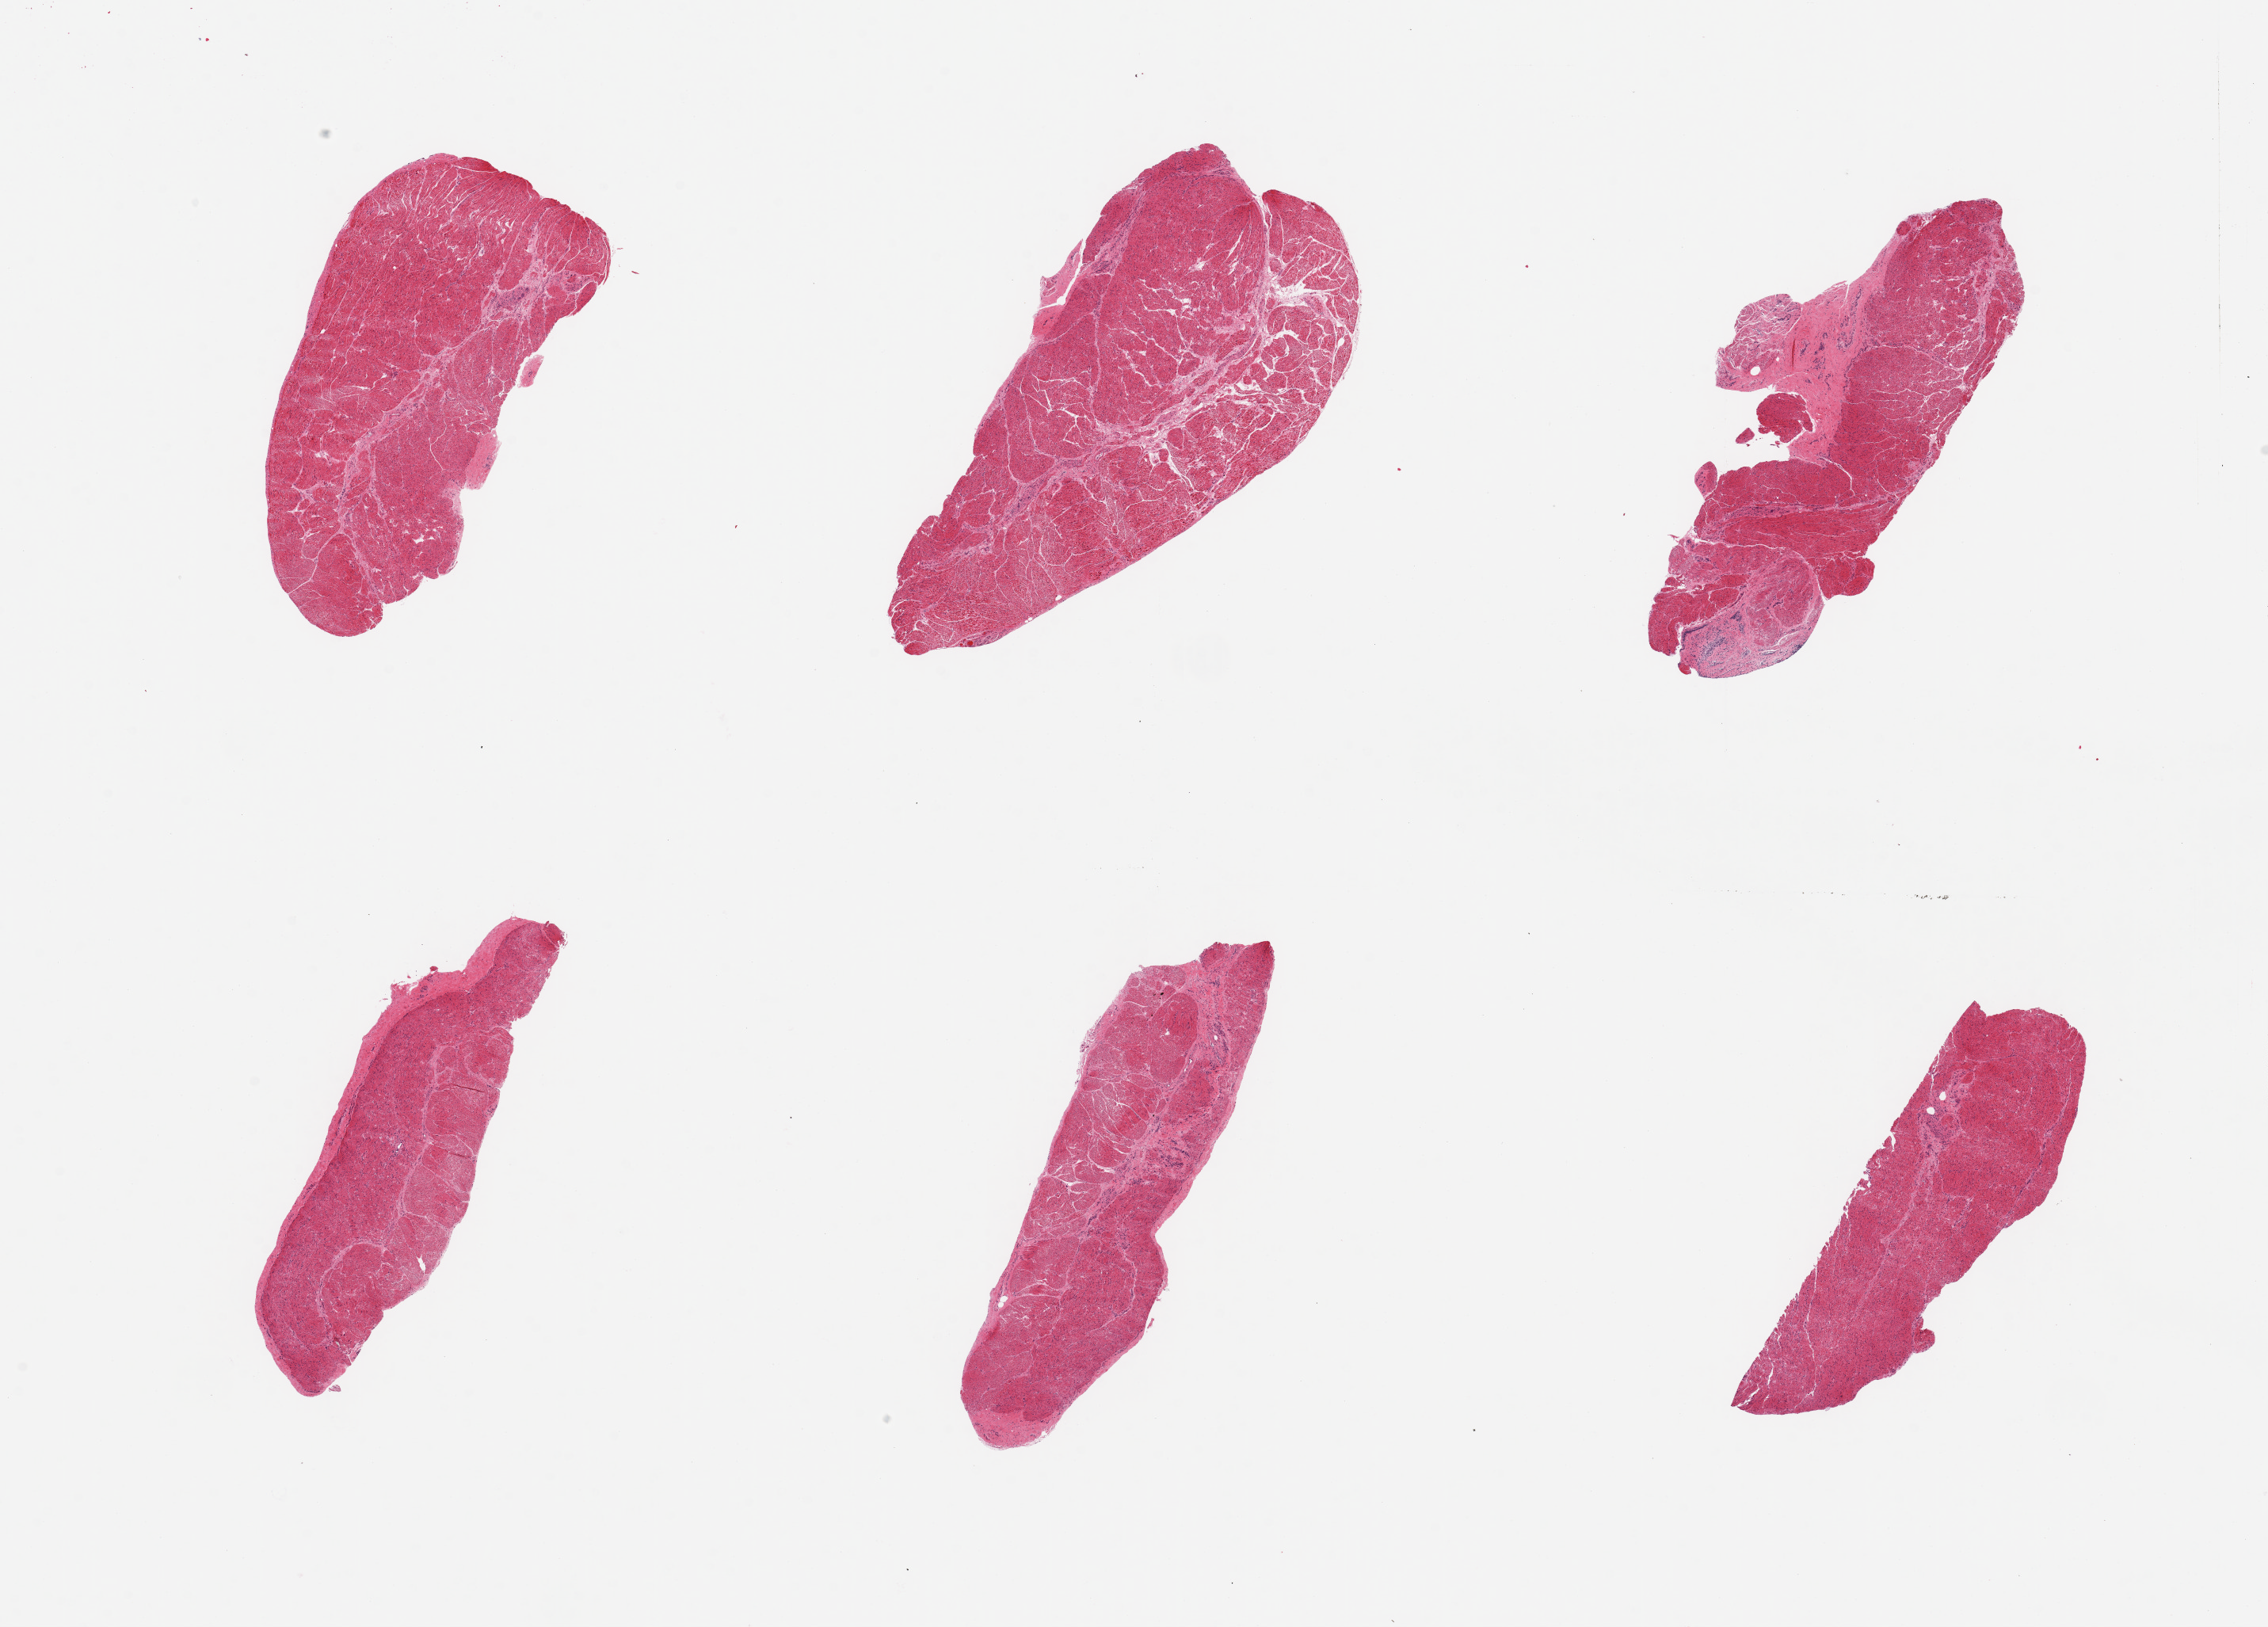
Whole-slide image, hematoxylin and eosin (H&E) stain, brightfield — a low-resolution overview of the entire scanned area, about 22.6 x 16.2 mm (acquisition: 20x scan), PAXgene-fixed, paraffin-embedded tissue, sampled site (target tissue): gastroesophageal junction, donor tissue sample. Donor: male.
Reviewer comment on this tissue sample: 6 pieces; predominantly target muscularis.